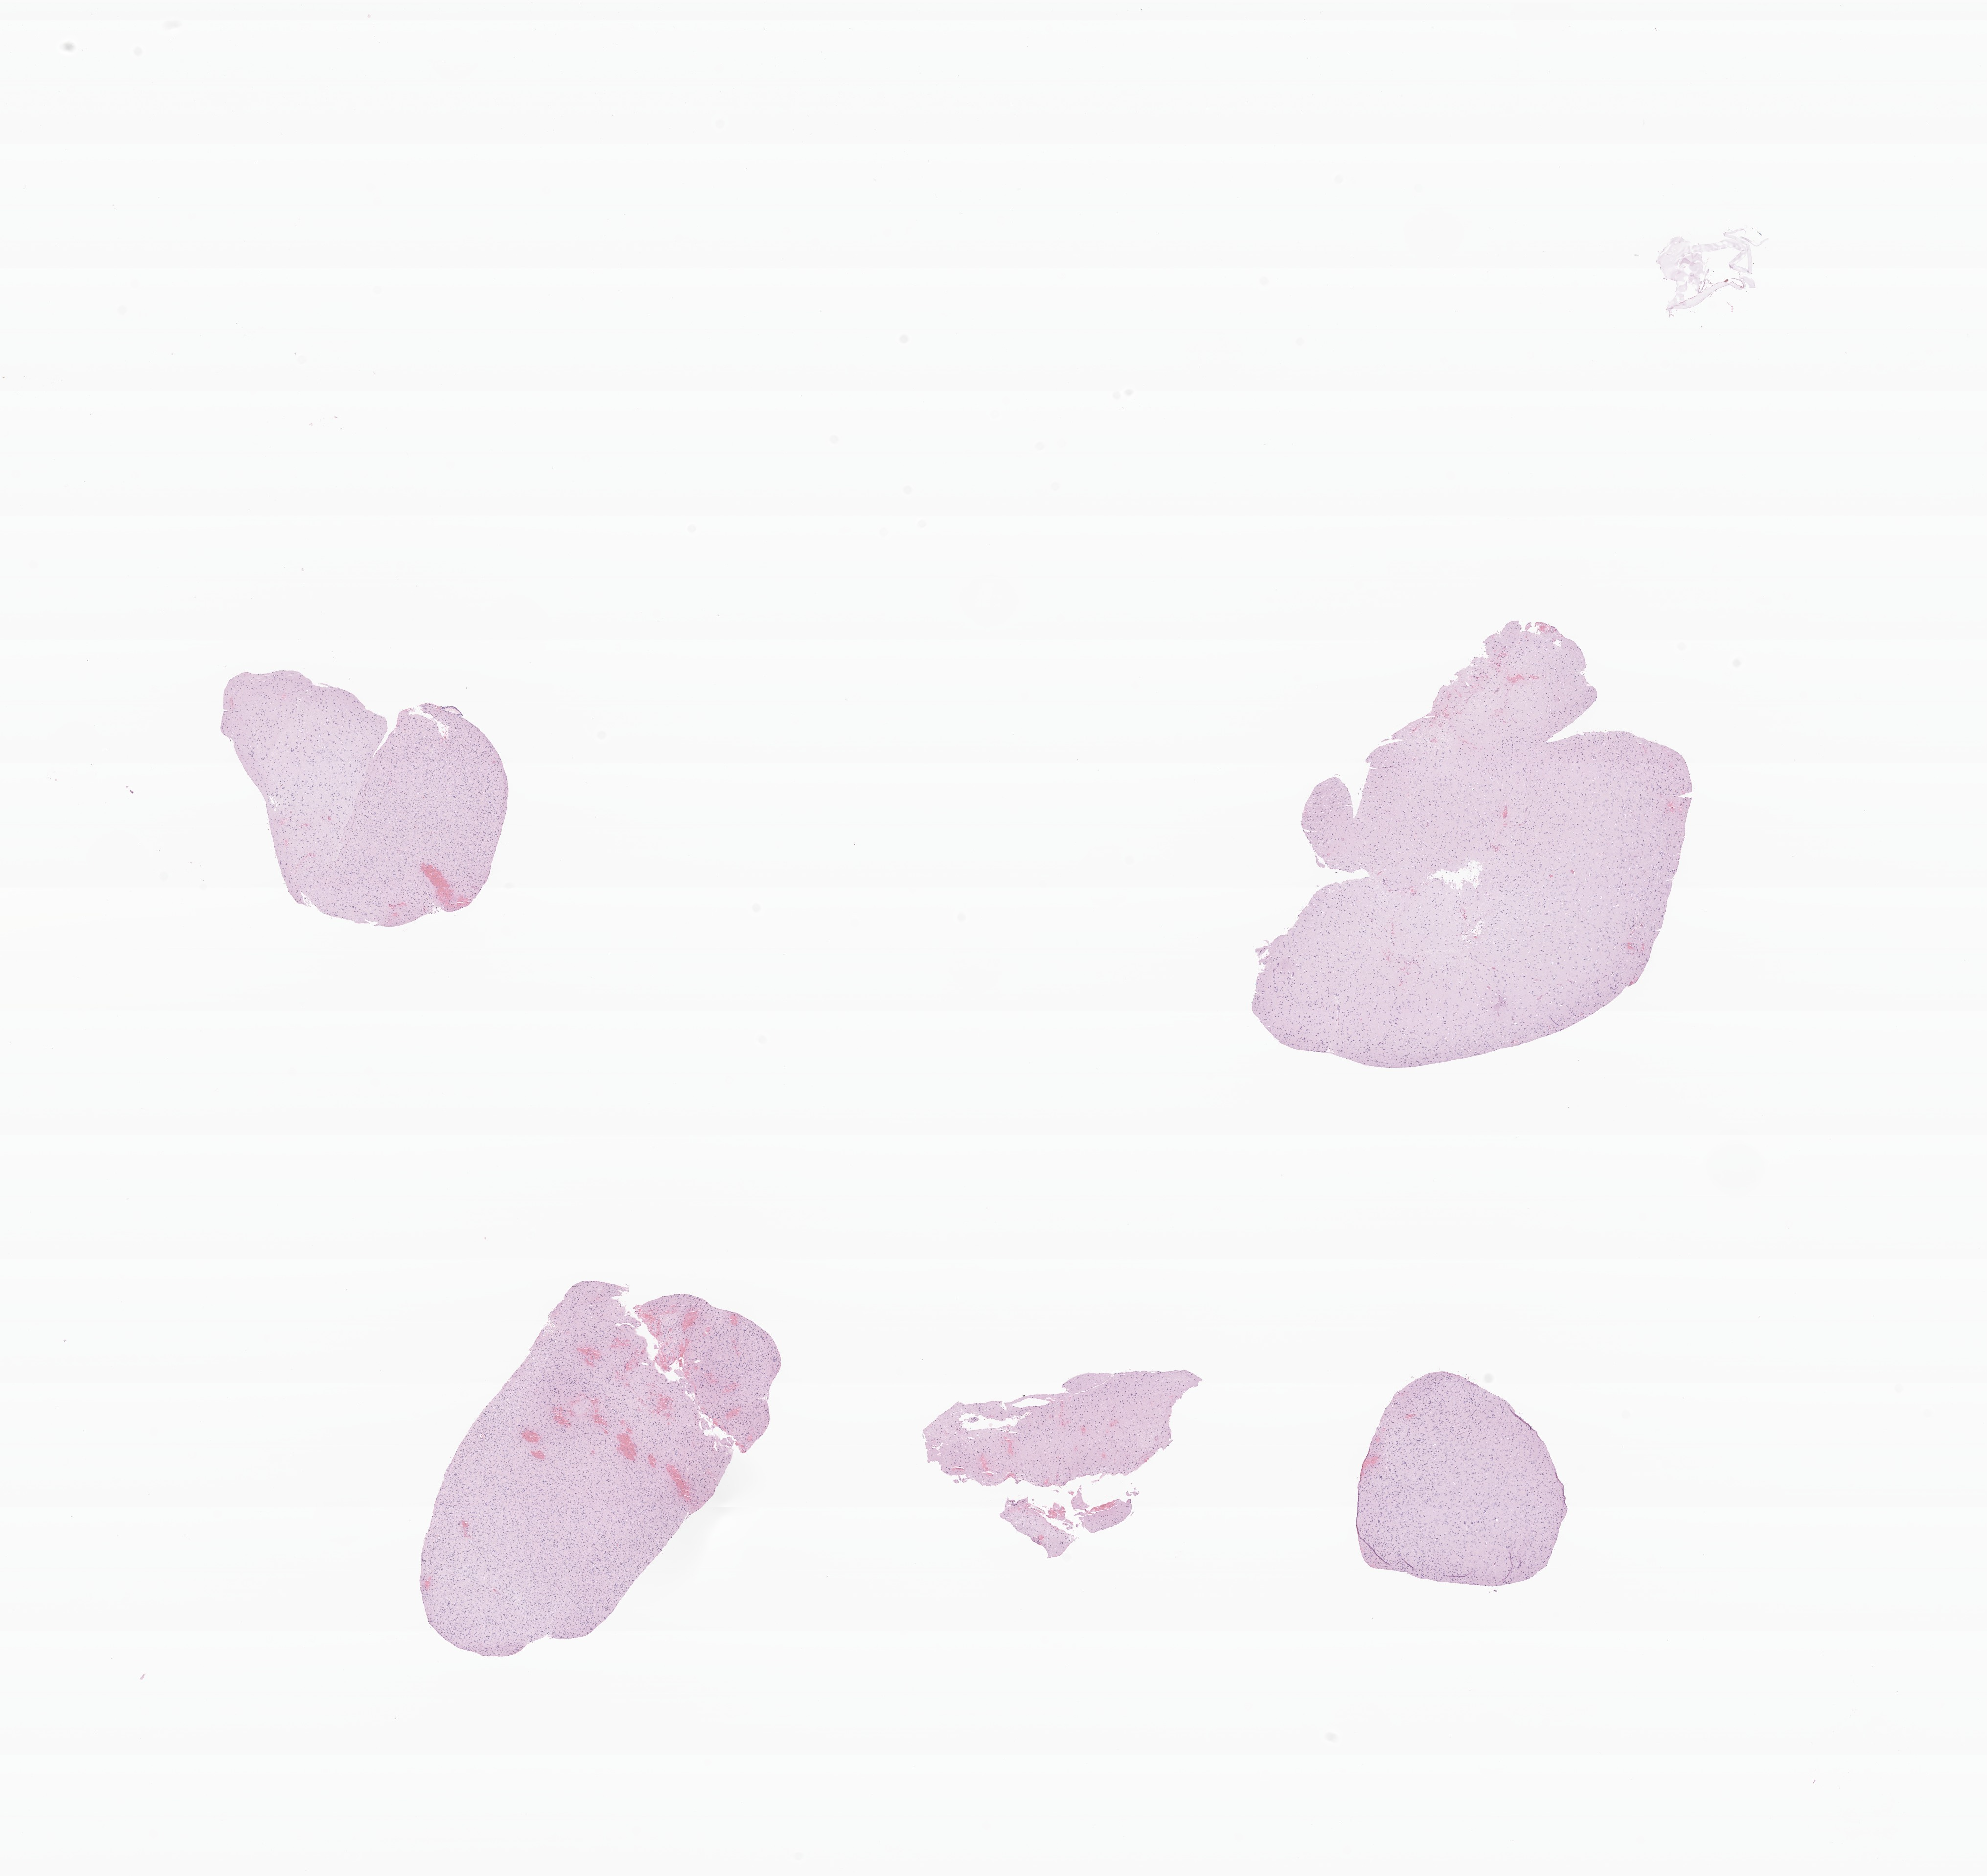
Digitized haematoxylin and eosin-stained section of tumor tissue from the temporal lobe, shown as a low-resolution overview of the whole scanned area (about 17.1 x 16.1 mm). FFPE section. Female patient, age 195 months (16 years 3 months).
Diagnosis (ICD-O-3 morphology term): Glioma, malignant.